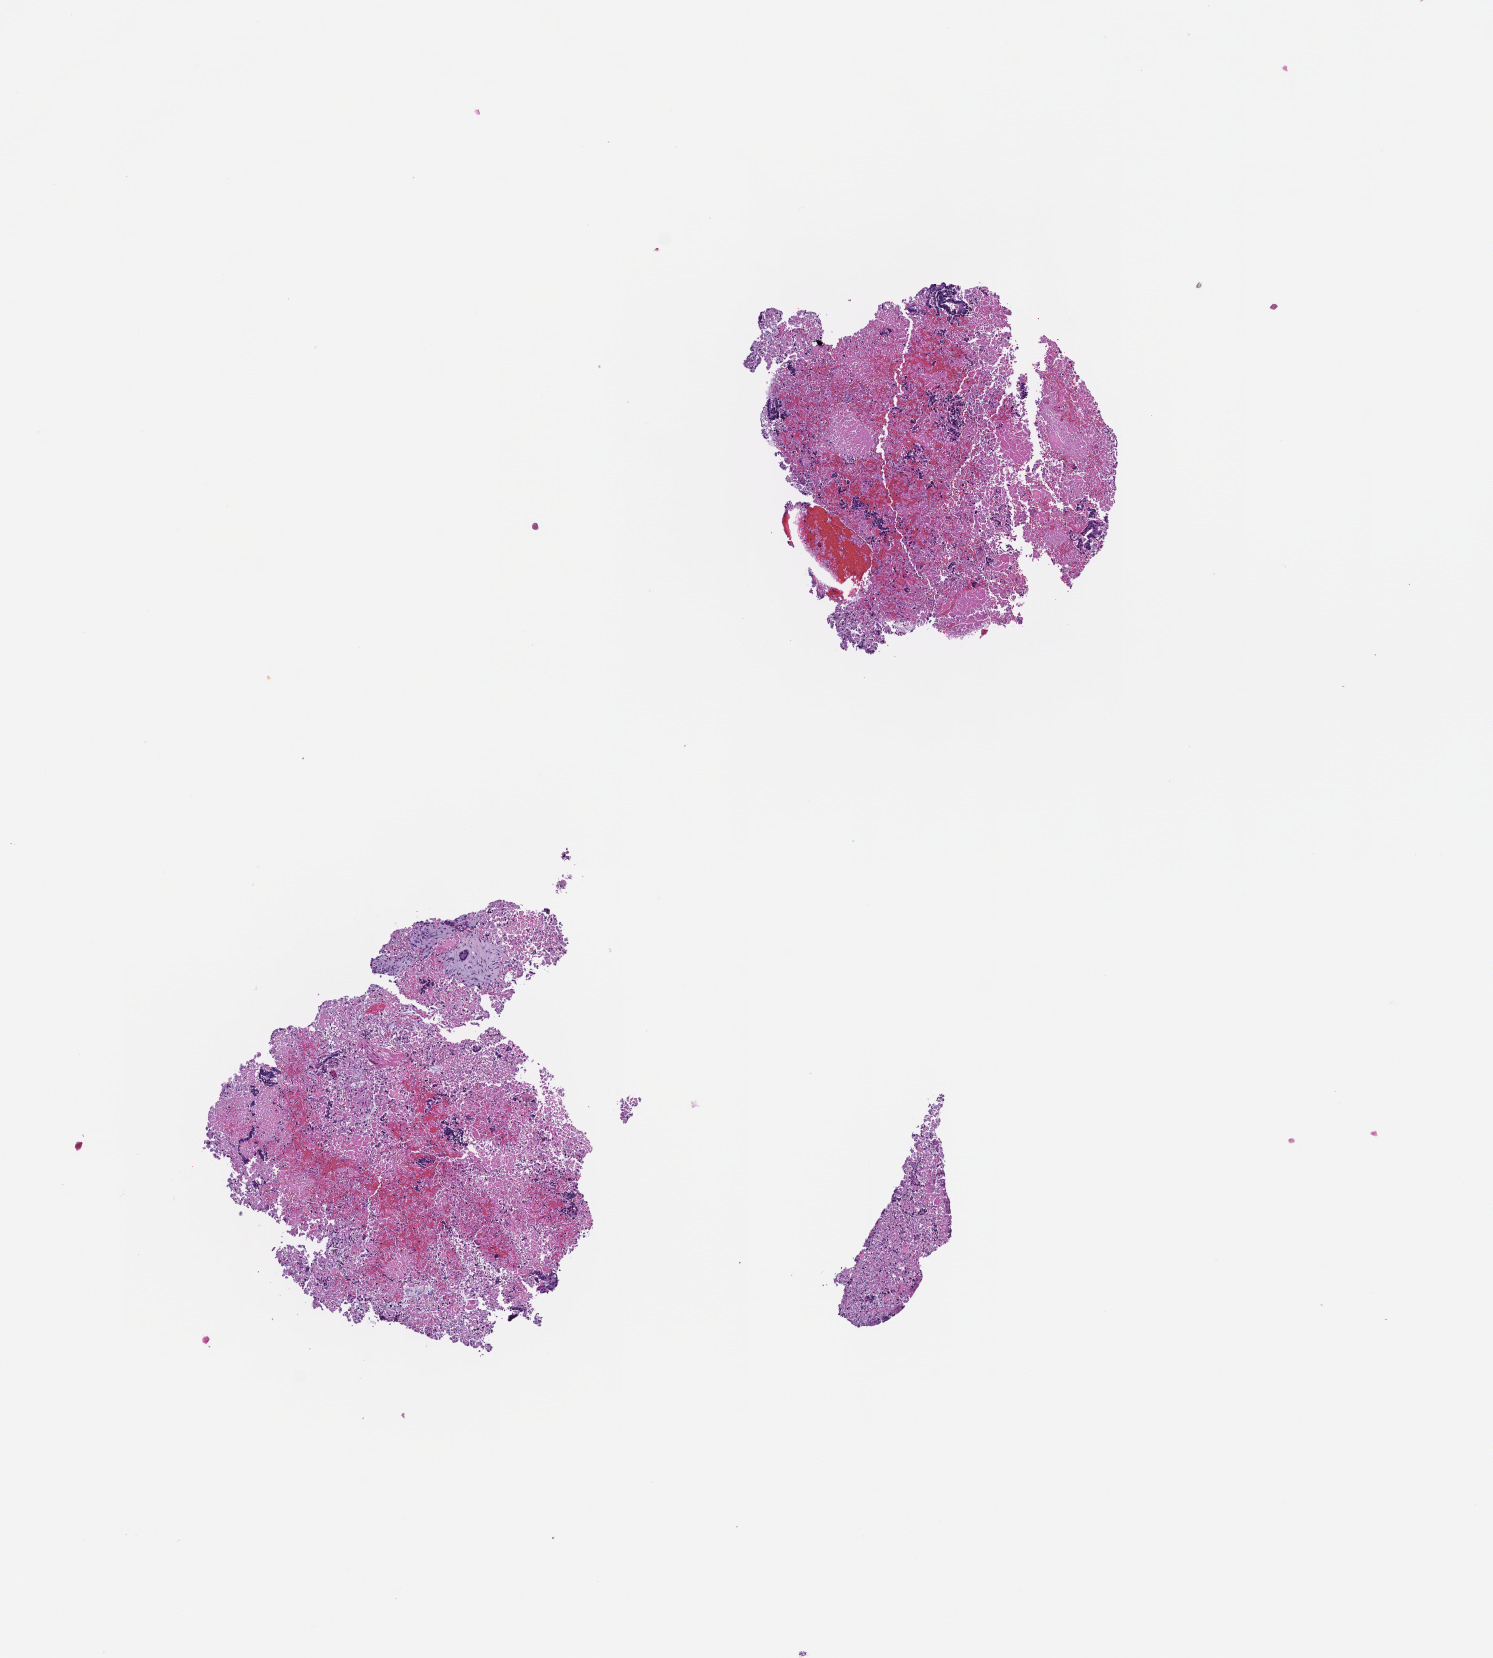
Whole-slide image, H&E stain, low-resolution overview of the scanned area, about 6.0 x 6.7 mm; formalin-fixed, paraffin-embedded (FFPE) tissue; archival tissue. Male patient.
This section: metastasis (sampled organ not recorded). Patient diagnosis (primary): Colorectal Carcinoma.